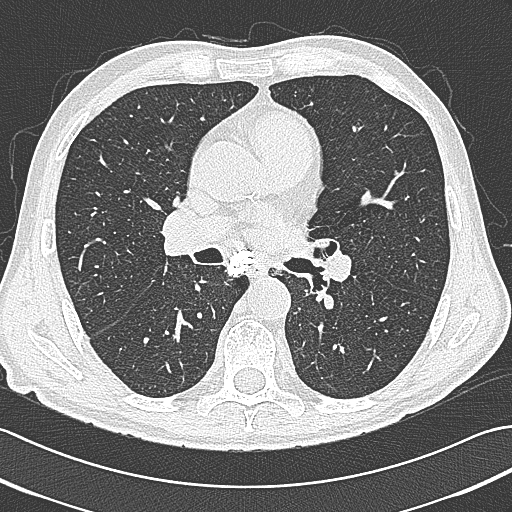
Low-dose screening chest CT, axial slice, baseline screening round, lung window (W 1500 / L -600 HU), lung (sharp) reconstruction kernel (B80f), slice 175 of 380 in the series, 512 × 512 image matrix, field of view 350 × 350 mm. Male participant, aged 65 years at enrolment.
- Lesion marked by an expert reader, bounding box [x1, y1, x2, y2] px = [303, 230, 346, 278].
- No non-calcified nodule or mass ≥4 mm was recorded by the screening reader at this exam.
- Official screen result: negative screen, minor abnormalities not suspicious for lung cancer.
- Later outcome: lung cancer diagnosed 161 days after this screen — large cell neuroendocrine carcinoma, left hilum, left main stem bronchus, stage IIIB (AJCC 6th edition), 70 mm at pathology.